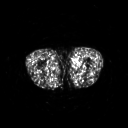
FDG PET of an extremity soft-tissue mass (from a PET/CT study), one axial slice; position 229 of 311 along the scan axis; 3.27 mm slice thickness; 128 × 128 image matrix, field of view 500 × 500 mm. Male patient, age 29 years. Case-level facts recorded for this patient, not image findings: histological type: mixoid liposarcoma; grade: low; site of the primary tumour: left thigh.
Outlined on this slice (expert contour drawn on MRI and transferred to this co-registered scan by the dataset authors):
- gross tumour volume (mass): bounding box <73,57,80,64> (left, top, right, bottom; pixels)